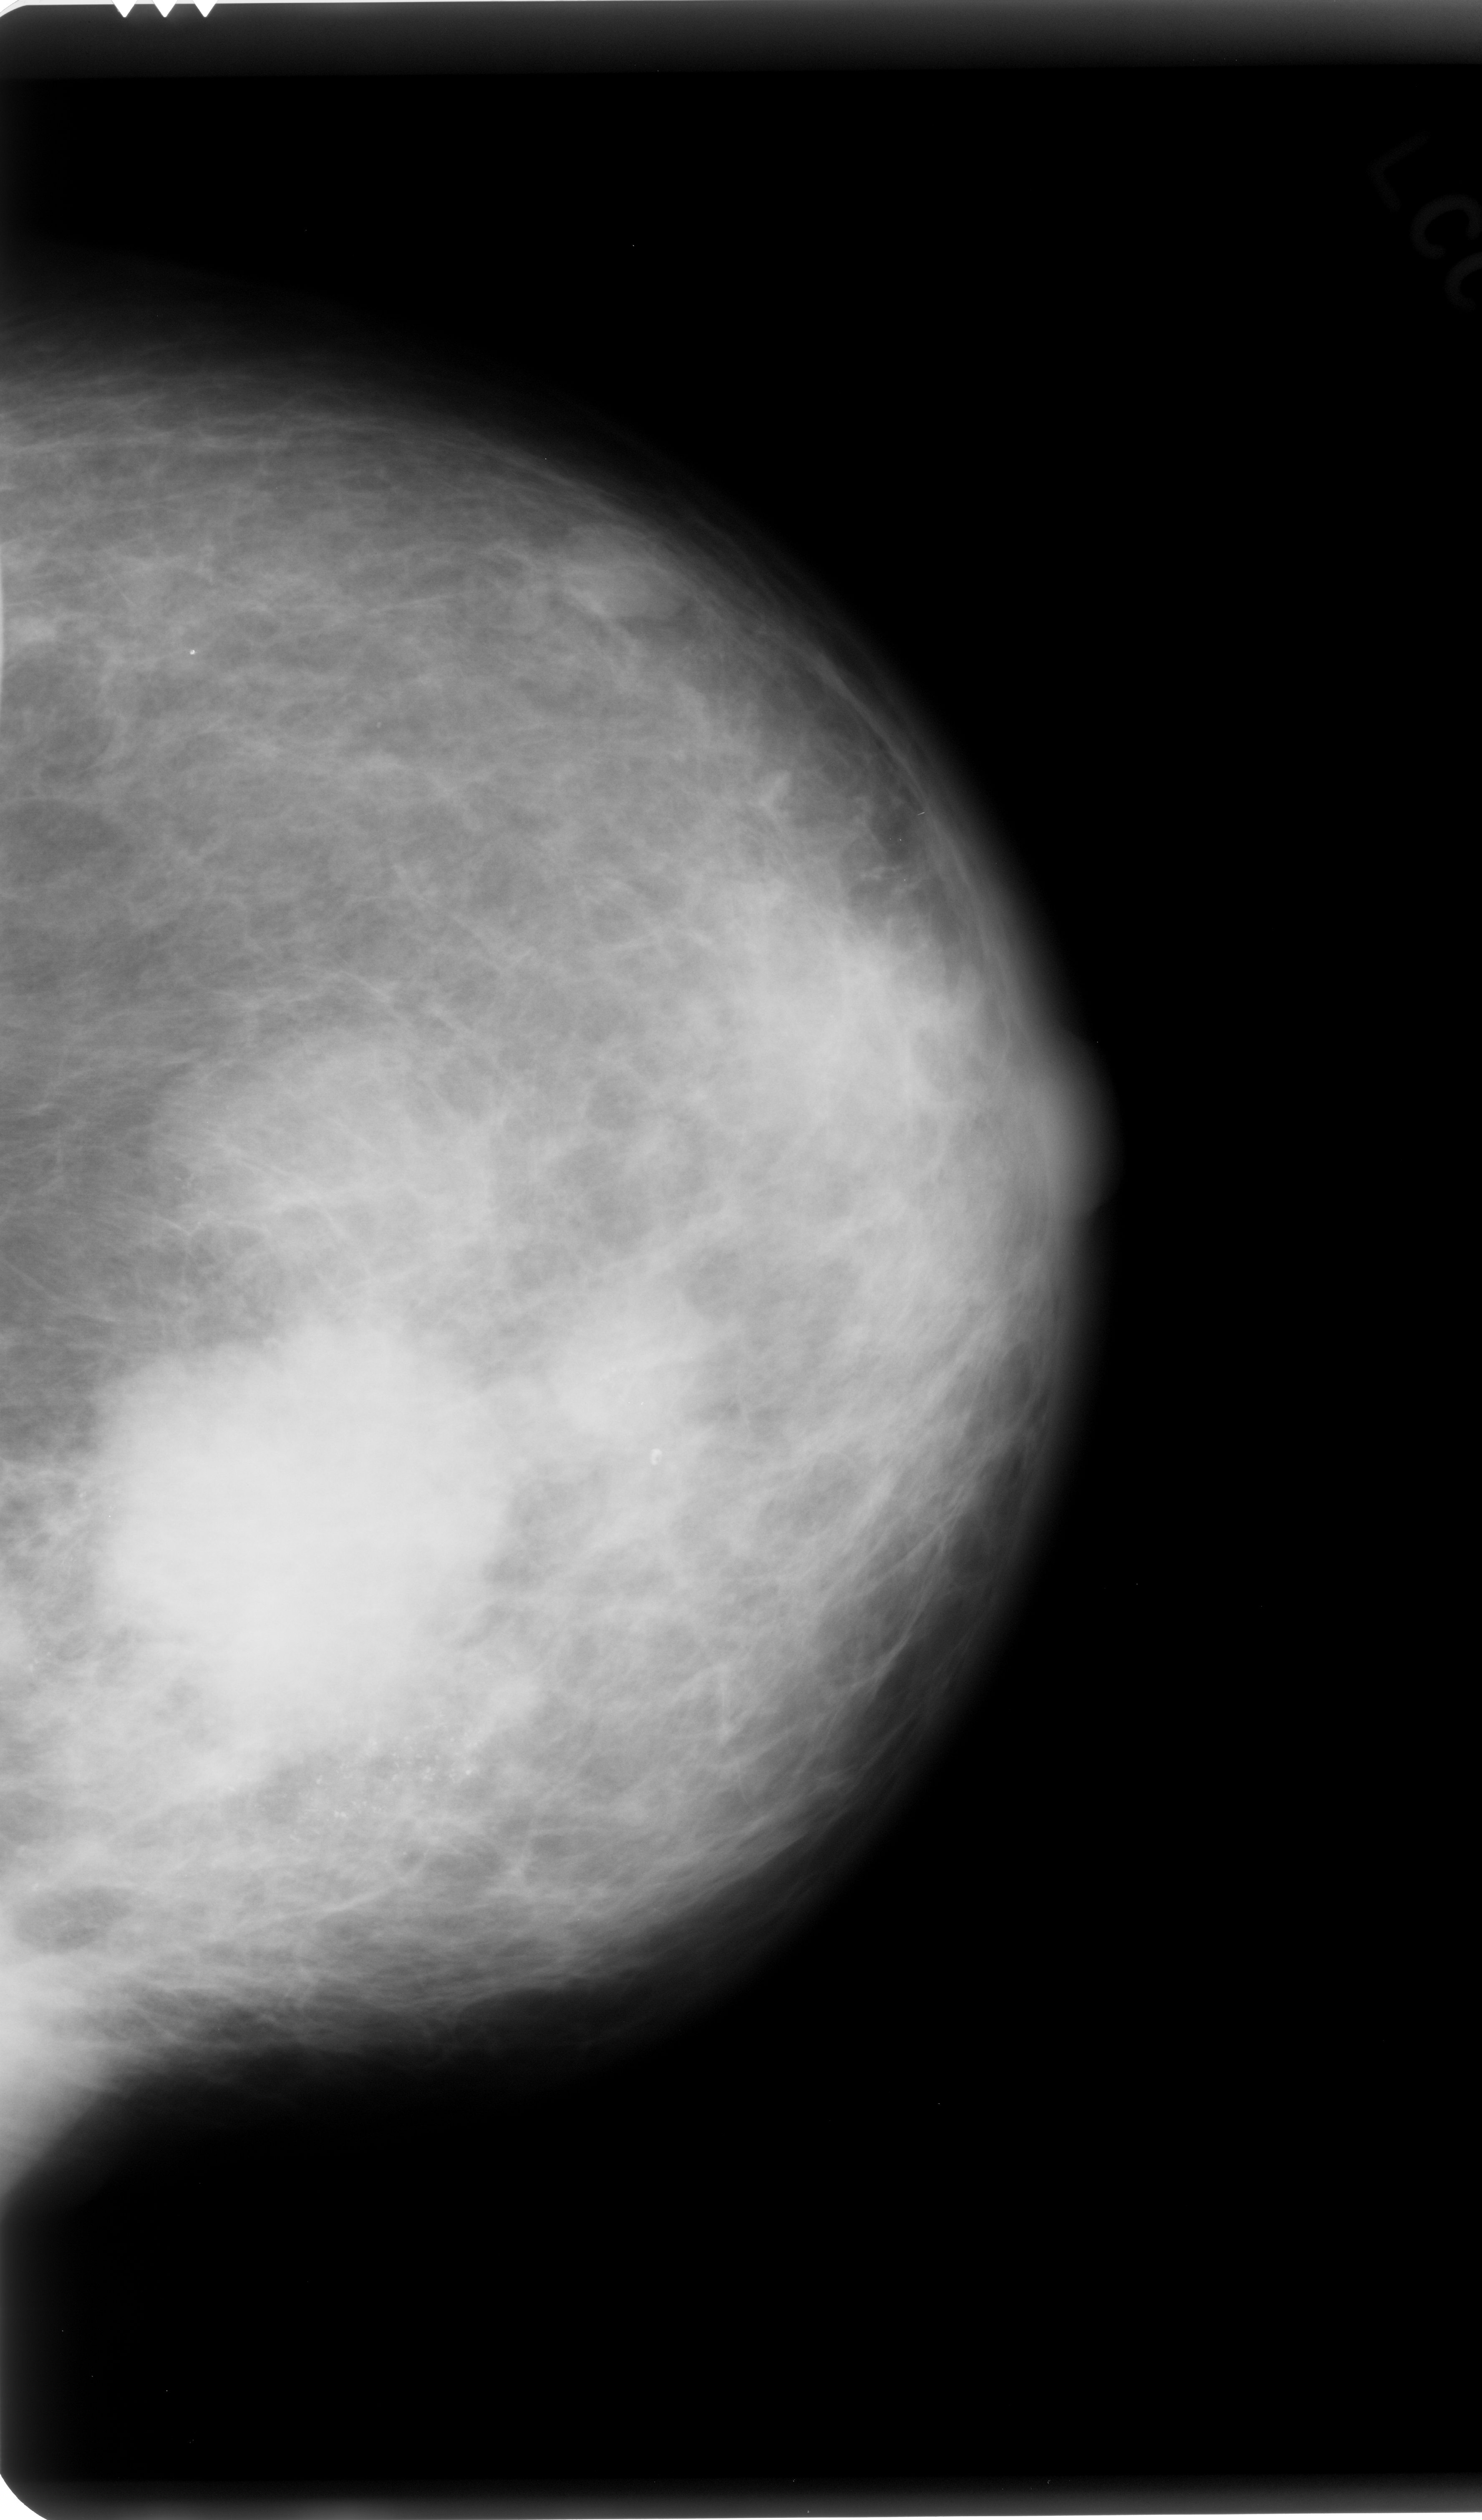
Scanned film-screen mammogram. Left breast. Craniocaudal (CC) view. Breast composition: scattered fibroglandular densities (BI-RADS density category 2 of 4). 1482 × 2520 image matrix.
Marked abnormalities (boxes around the expert regions of interest):
- calcifications, morphology pleomorphic, distribution segmental; BI-RADS assessment category 5; pathology (as recorded): malignant: bounding box <0,864,1159,2114> (left, top, right, bottom; pixels)